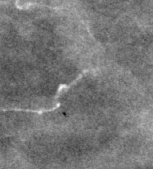
Crop from a digitized film mammogram around one marked abnormality, right breast, CC view, BI-RADS breast density category 1 (scale 1–4).
Calcifications, morphology fine linear branching; BI-RADS assessment category 2; subtlety rating 4 on a 1 (subtle) to 5 (obvious) scale; benign without callback (not worked up further).